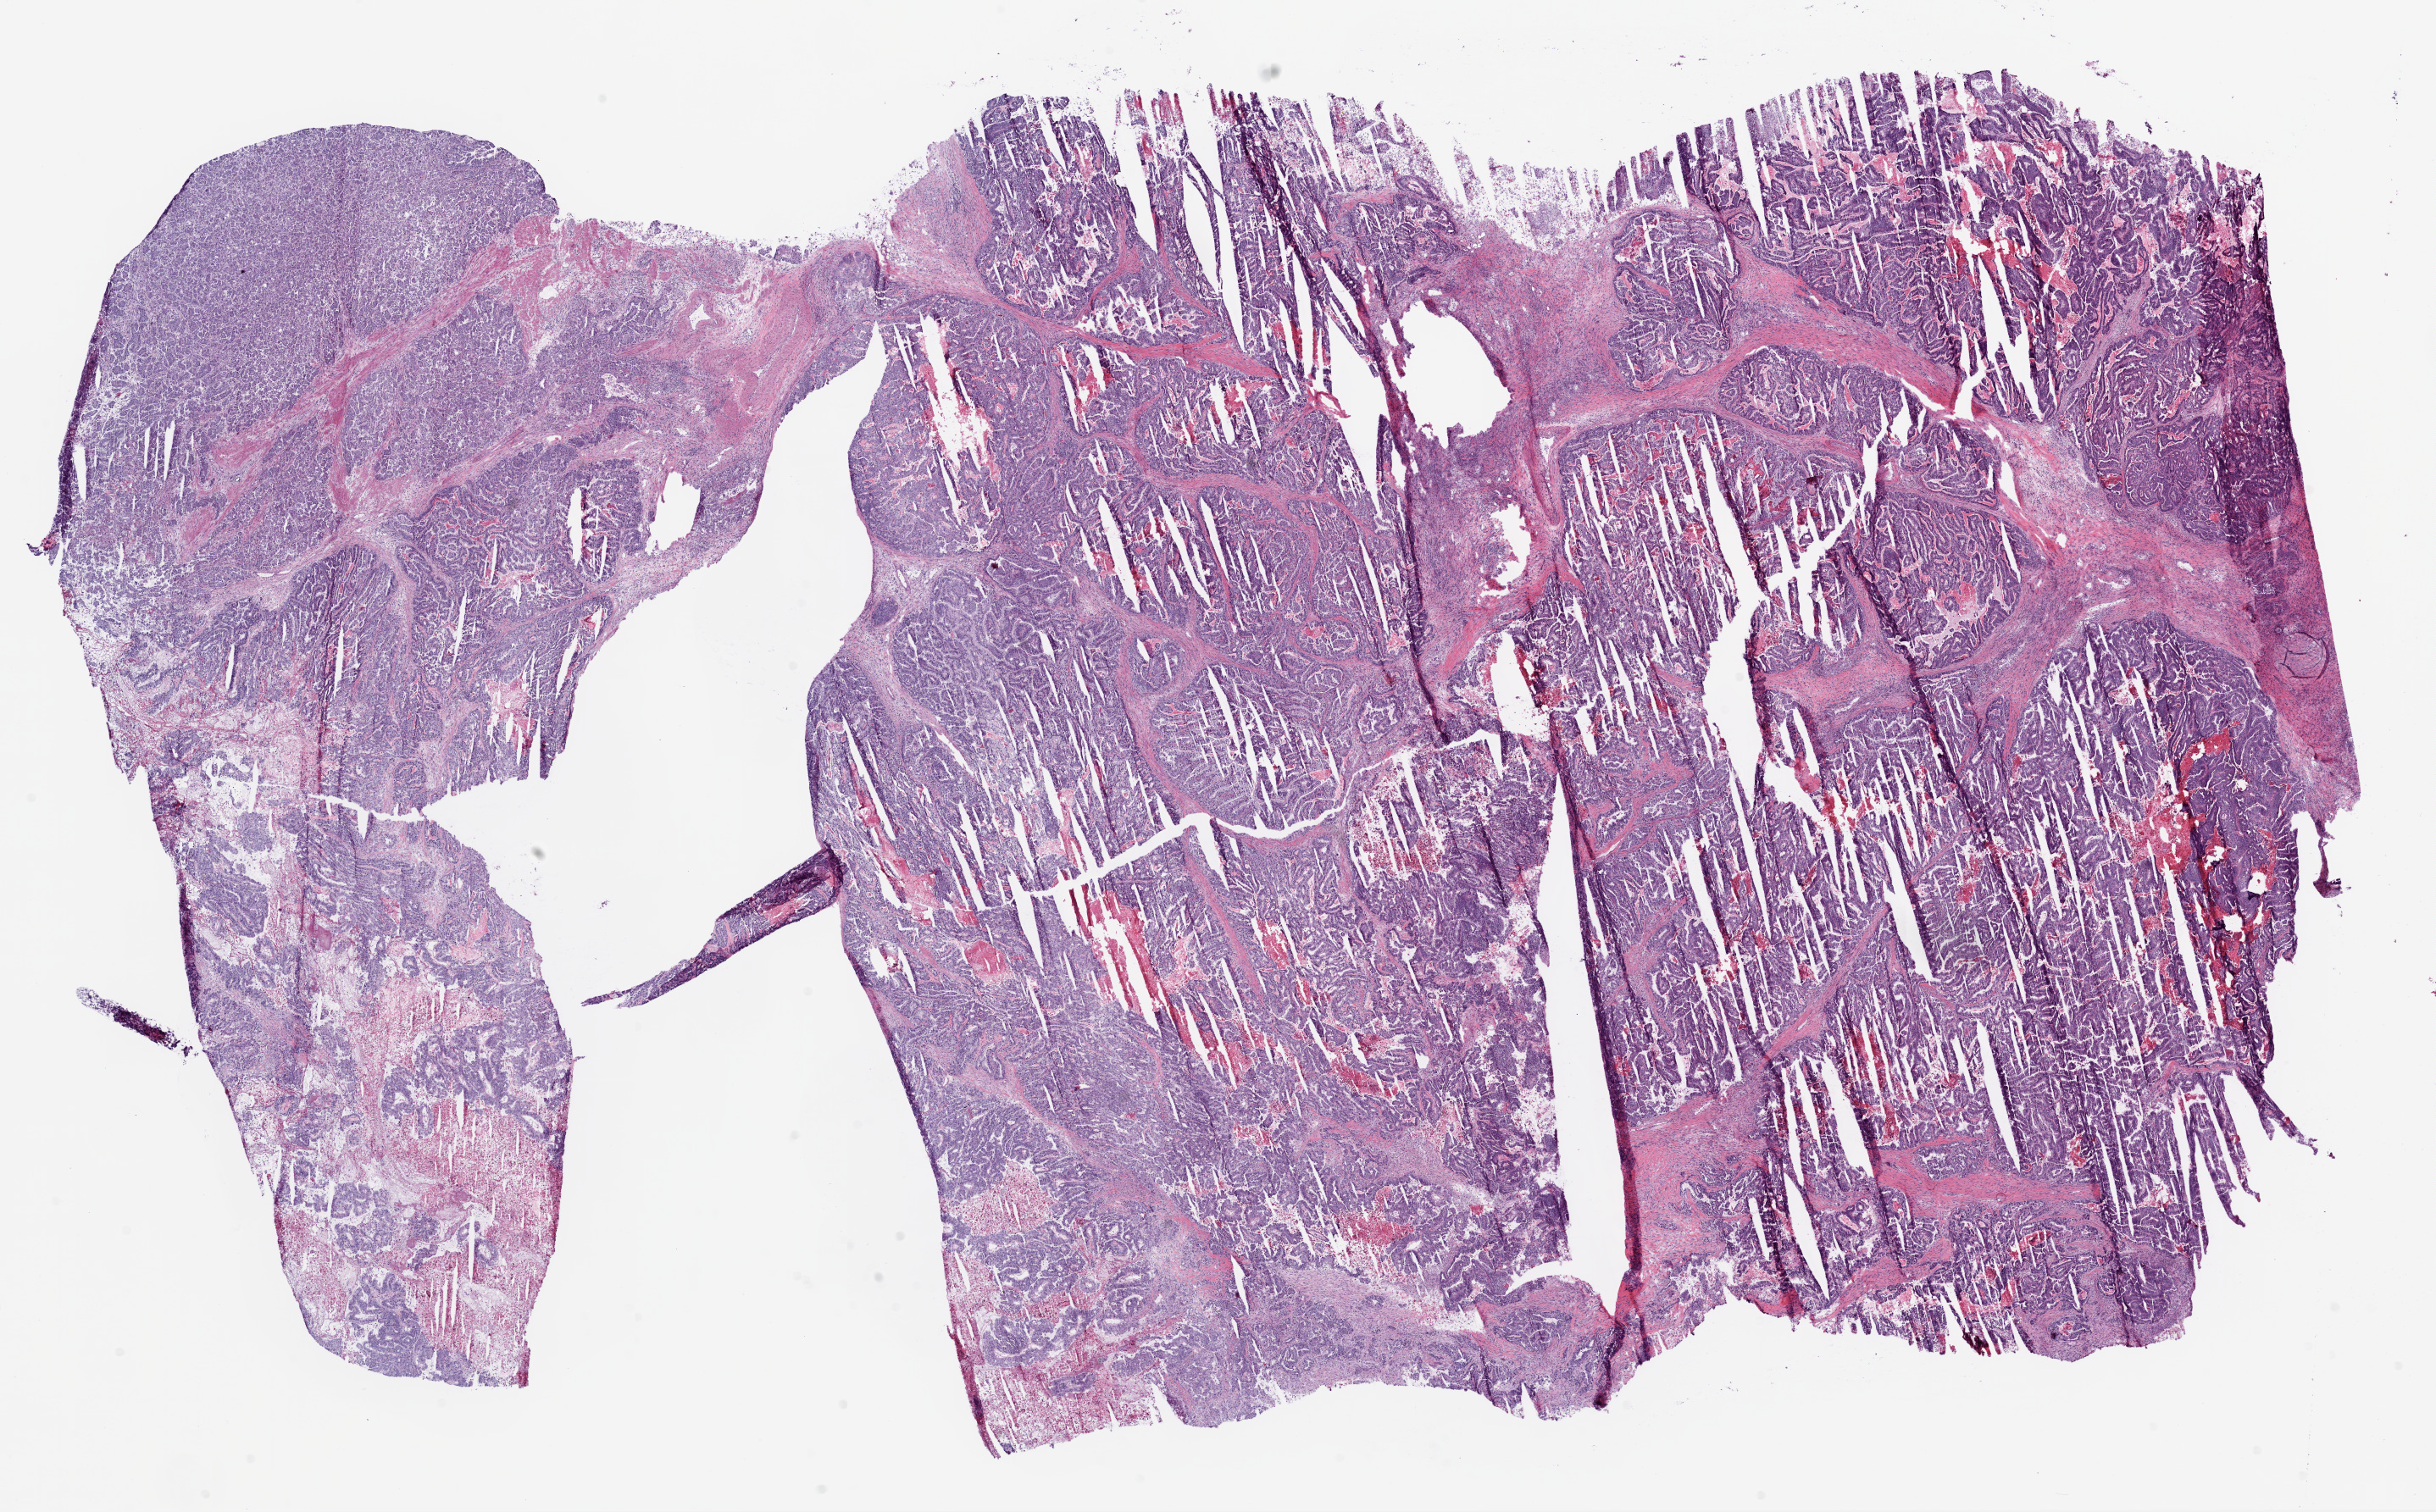
H&E whole-slide image, a low-resolution overview of the entire scanned area, about 23.1 x 14.3 mm (slide scanned at 20x). Frozen section from the top of the tissue portion. Stomach, primary tumour sample. Male, age 87 years at initial diagnosis. Histologic grade: G2 (moderately differentiated). Composition of this section per pathologist review: tumour cells 80%, tumour nuclei 80%, normal cells 0%, stromal cells 10%, necrosis 10%.
- pathologic diagnosis: Adenocarcinoma, NOS (gastric antrum)